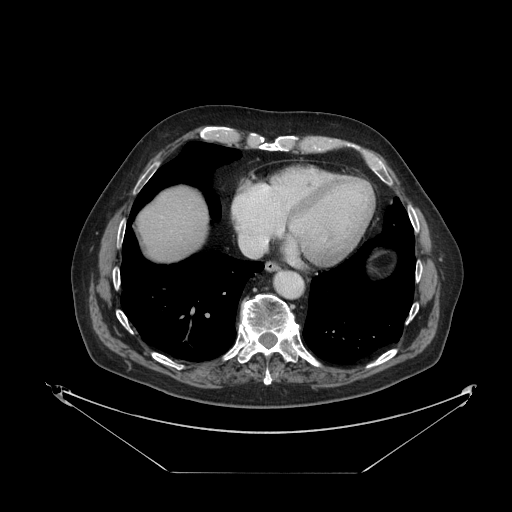
Contrast-enhanced abdominal CT, one axial slice; reconstruction kernel STANDARD; intravenous contrast given; soft-tissue window (W 400 / L 40 HU); 2.5 mm slice thickness; 512 × 512 image matrix, field of view 500 × 500 mm. Male patient, age 68 years. Case-level facts recorded for this patient, not image findings: diagnosis: colorectal cancer liver metastases, imaged before liver resection; multiple liver metastases: no; largest metastasis: 4 cm; disease in both lobes: no.
Outlined on this slice (expert manual segmentation):
- liver: bounding box <139,188,208,262> (left, top, right, bottom; pixels)
- planned liver remnant (the part of the liver to remain after resection): <138,188,208,262>